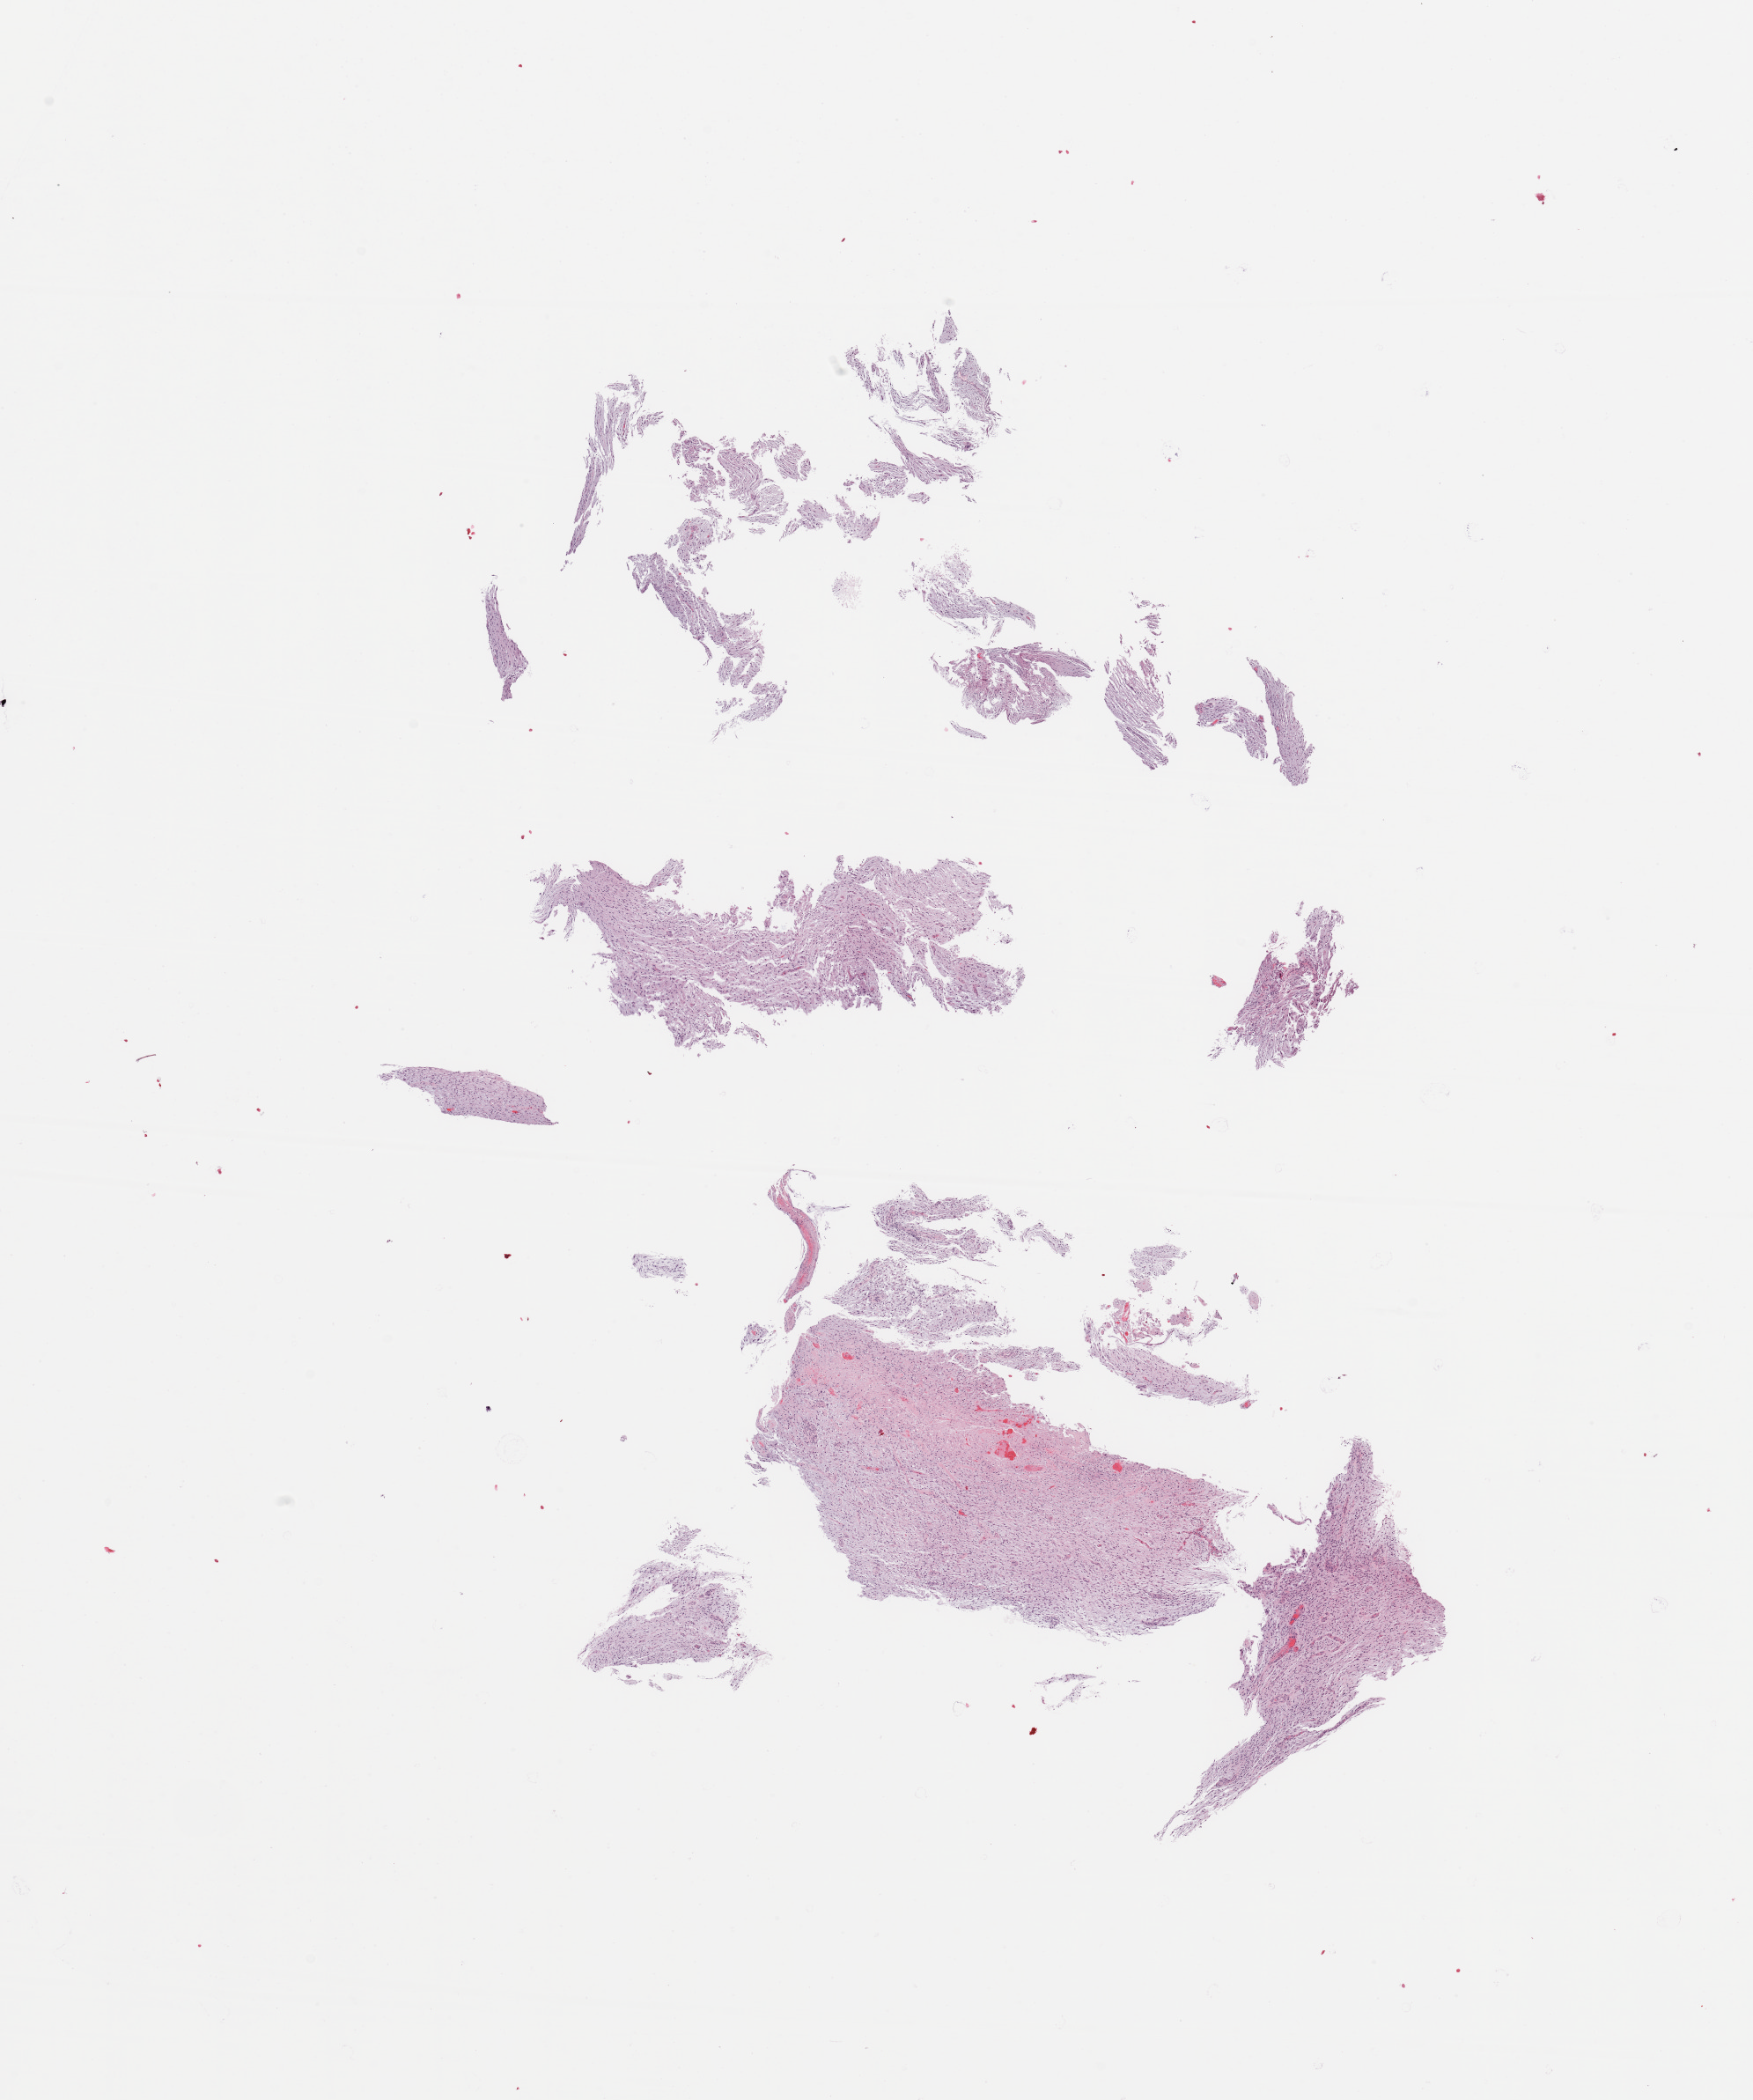
Whole-slide histology image, Hematoxylin and eosin (H&E) stained — whole scanned area (about 15.8 x 18.9 mm) shown as a low-resolution overview, tumour tissue sample, sampled site: frontal lobe. Female, 57 y/o. Pathologist review of this section (percent, as recorded): tumour nuclei 70%, necrosis 10%.
Histologic diagnosis: Glioblastoma.